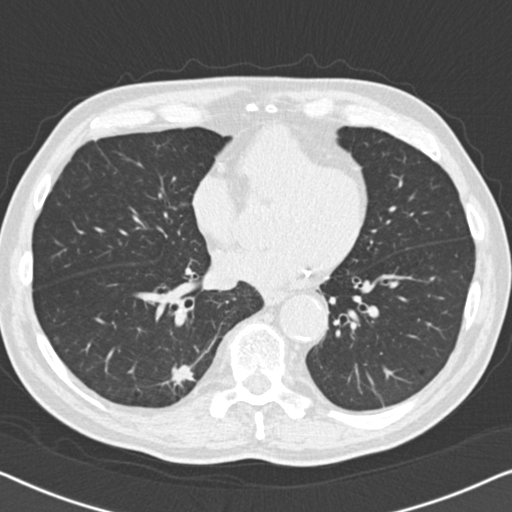
Low-dose screening chest CT, one axial slice. Slice 57 of 164 in the series (ordered by position). Reconstruction kernel B30f. Lung window (W 1500 / L -600 HU). 2 mm slice thickness. 512 × 512 image matrix, field of view 330 × 330 mm.
Annotated regions visible in this slice (outlined manually by an expert reader):
- lesion 1 (tumor, lower lobe of right lung): bounding box <169,365,196,386> (left, top, right, bottom; pixels)